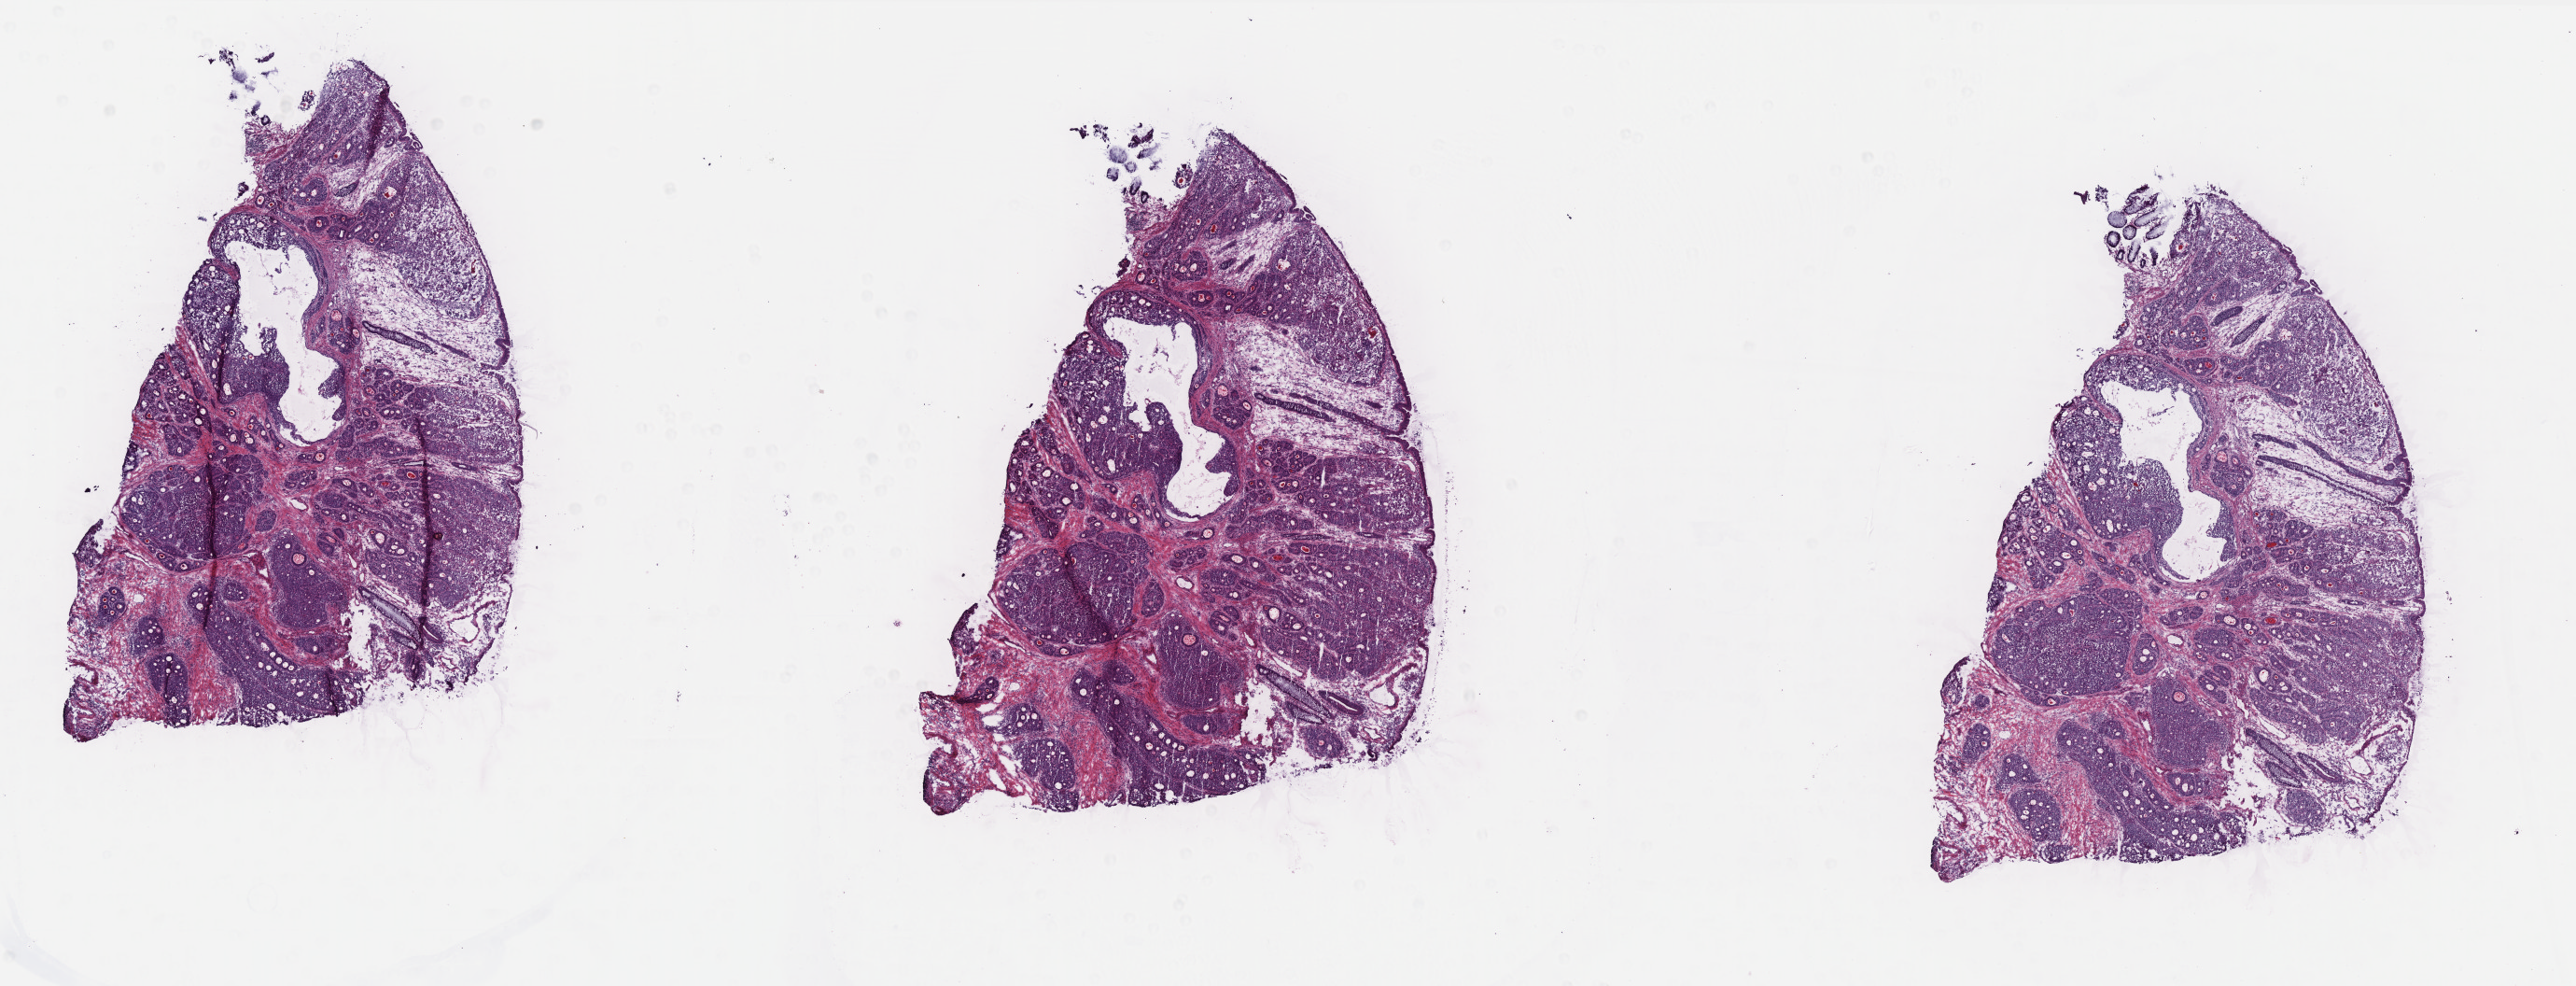
Digitized Hematoxylin and eosin (H&E) stained tissue section (whole slide), low-resolution overview of the scanned area, about 22.1 x 8.5 mm. Frozen section. Colon, primary tumour sample. Female, age 83 years at initial diagnosis. Pathologist review of this section (percent, as recorded): tumour cells 88%, tumour nuclei 85%, normal cells 3%, stromal cells 6%, necrosis 3%. Inflammatory infiltration, as recorded: lymphocyte infiltration 2%, monocyte infiltration 2%, neutrophil infiltration 0%.
Lymph nodes positive (case pathology): 32 of 40 examined. Diagnosis: Adenocarcinoma, NOS. TNM: T3 N2 M0. AJCC pathologic stage: IIIC (6th edition).